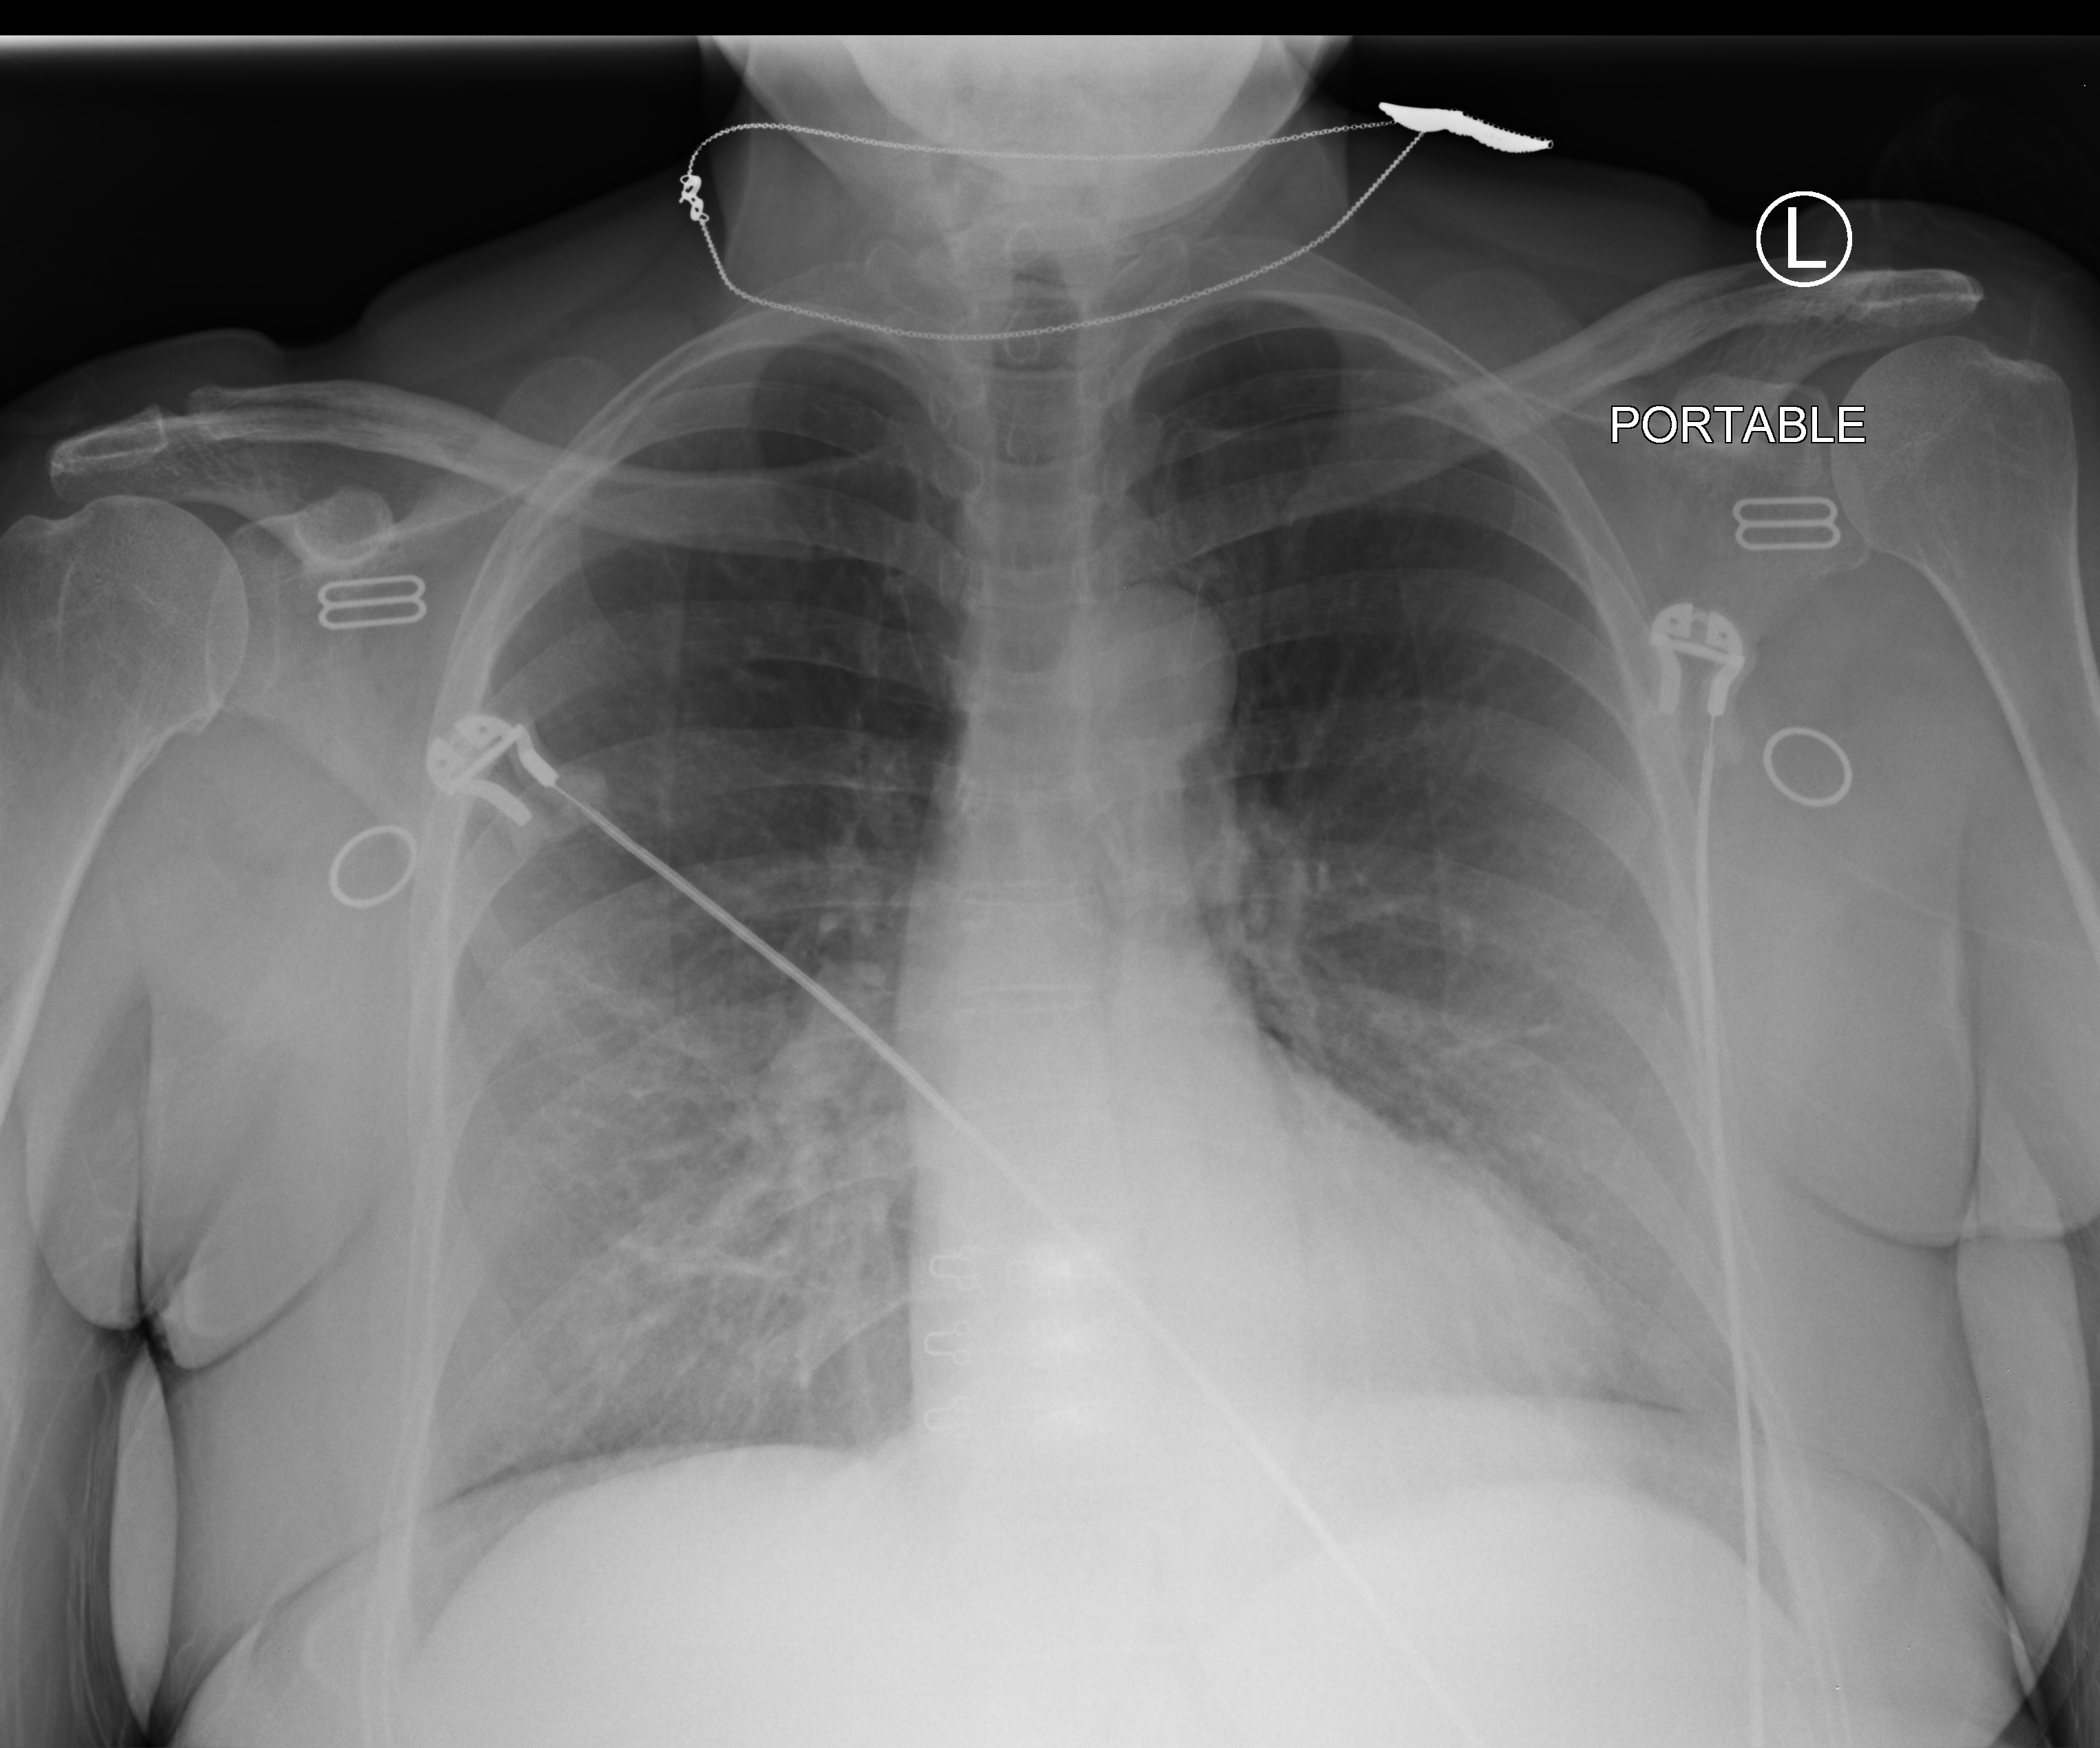
Portable chest radiograph, anteroposterior (AP) projection. Female patient hospitalised with COVID-19, age 60–74 years.
From the hospital-stay record, not from the radiograph (when in the stay this image was taken is not recorded):
- admitted to intensive care during this hospital stay: no